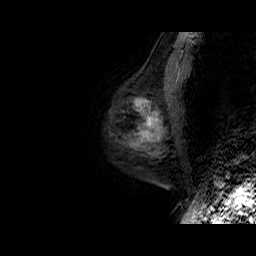
Breast MRI (dynamic contrast-enhanced), one sagittal slice. Position 15 of 50 along the scan axis. Dynamic contrast-enhanced series, time point 2 of 6 at this slice position (early post-contrast). 1.5 T. TE 6.5 ms, TR 32.9 ms. 4 mm slice thickness. 256 × 256 image matrix, field of view 200 × 200 mm. Female patient. Case-level facts recorded for this patient, not image findings: setting: breast cancer imaged before/during neoadjuvant chemotherapy; receptor status: HR-positive, HER2-negative.
Structures marked on this image (semi-automatically segmented with operator editing):
- analysis volume of interest (the breast-tissue region the enhancement analysis was run in; not a lesion): bounding box [x1, y1, x2, y2] px = [114, 75, 179, 149]
- tumour enhancement mask (voxels above the 100 % enhancement threshold inside the analysis volume of interest): [134, 101, 160, 141]